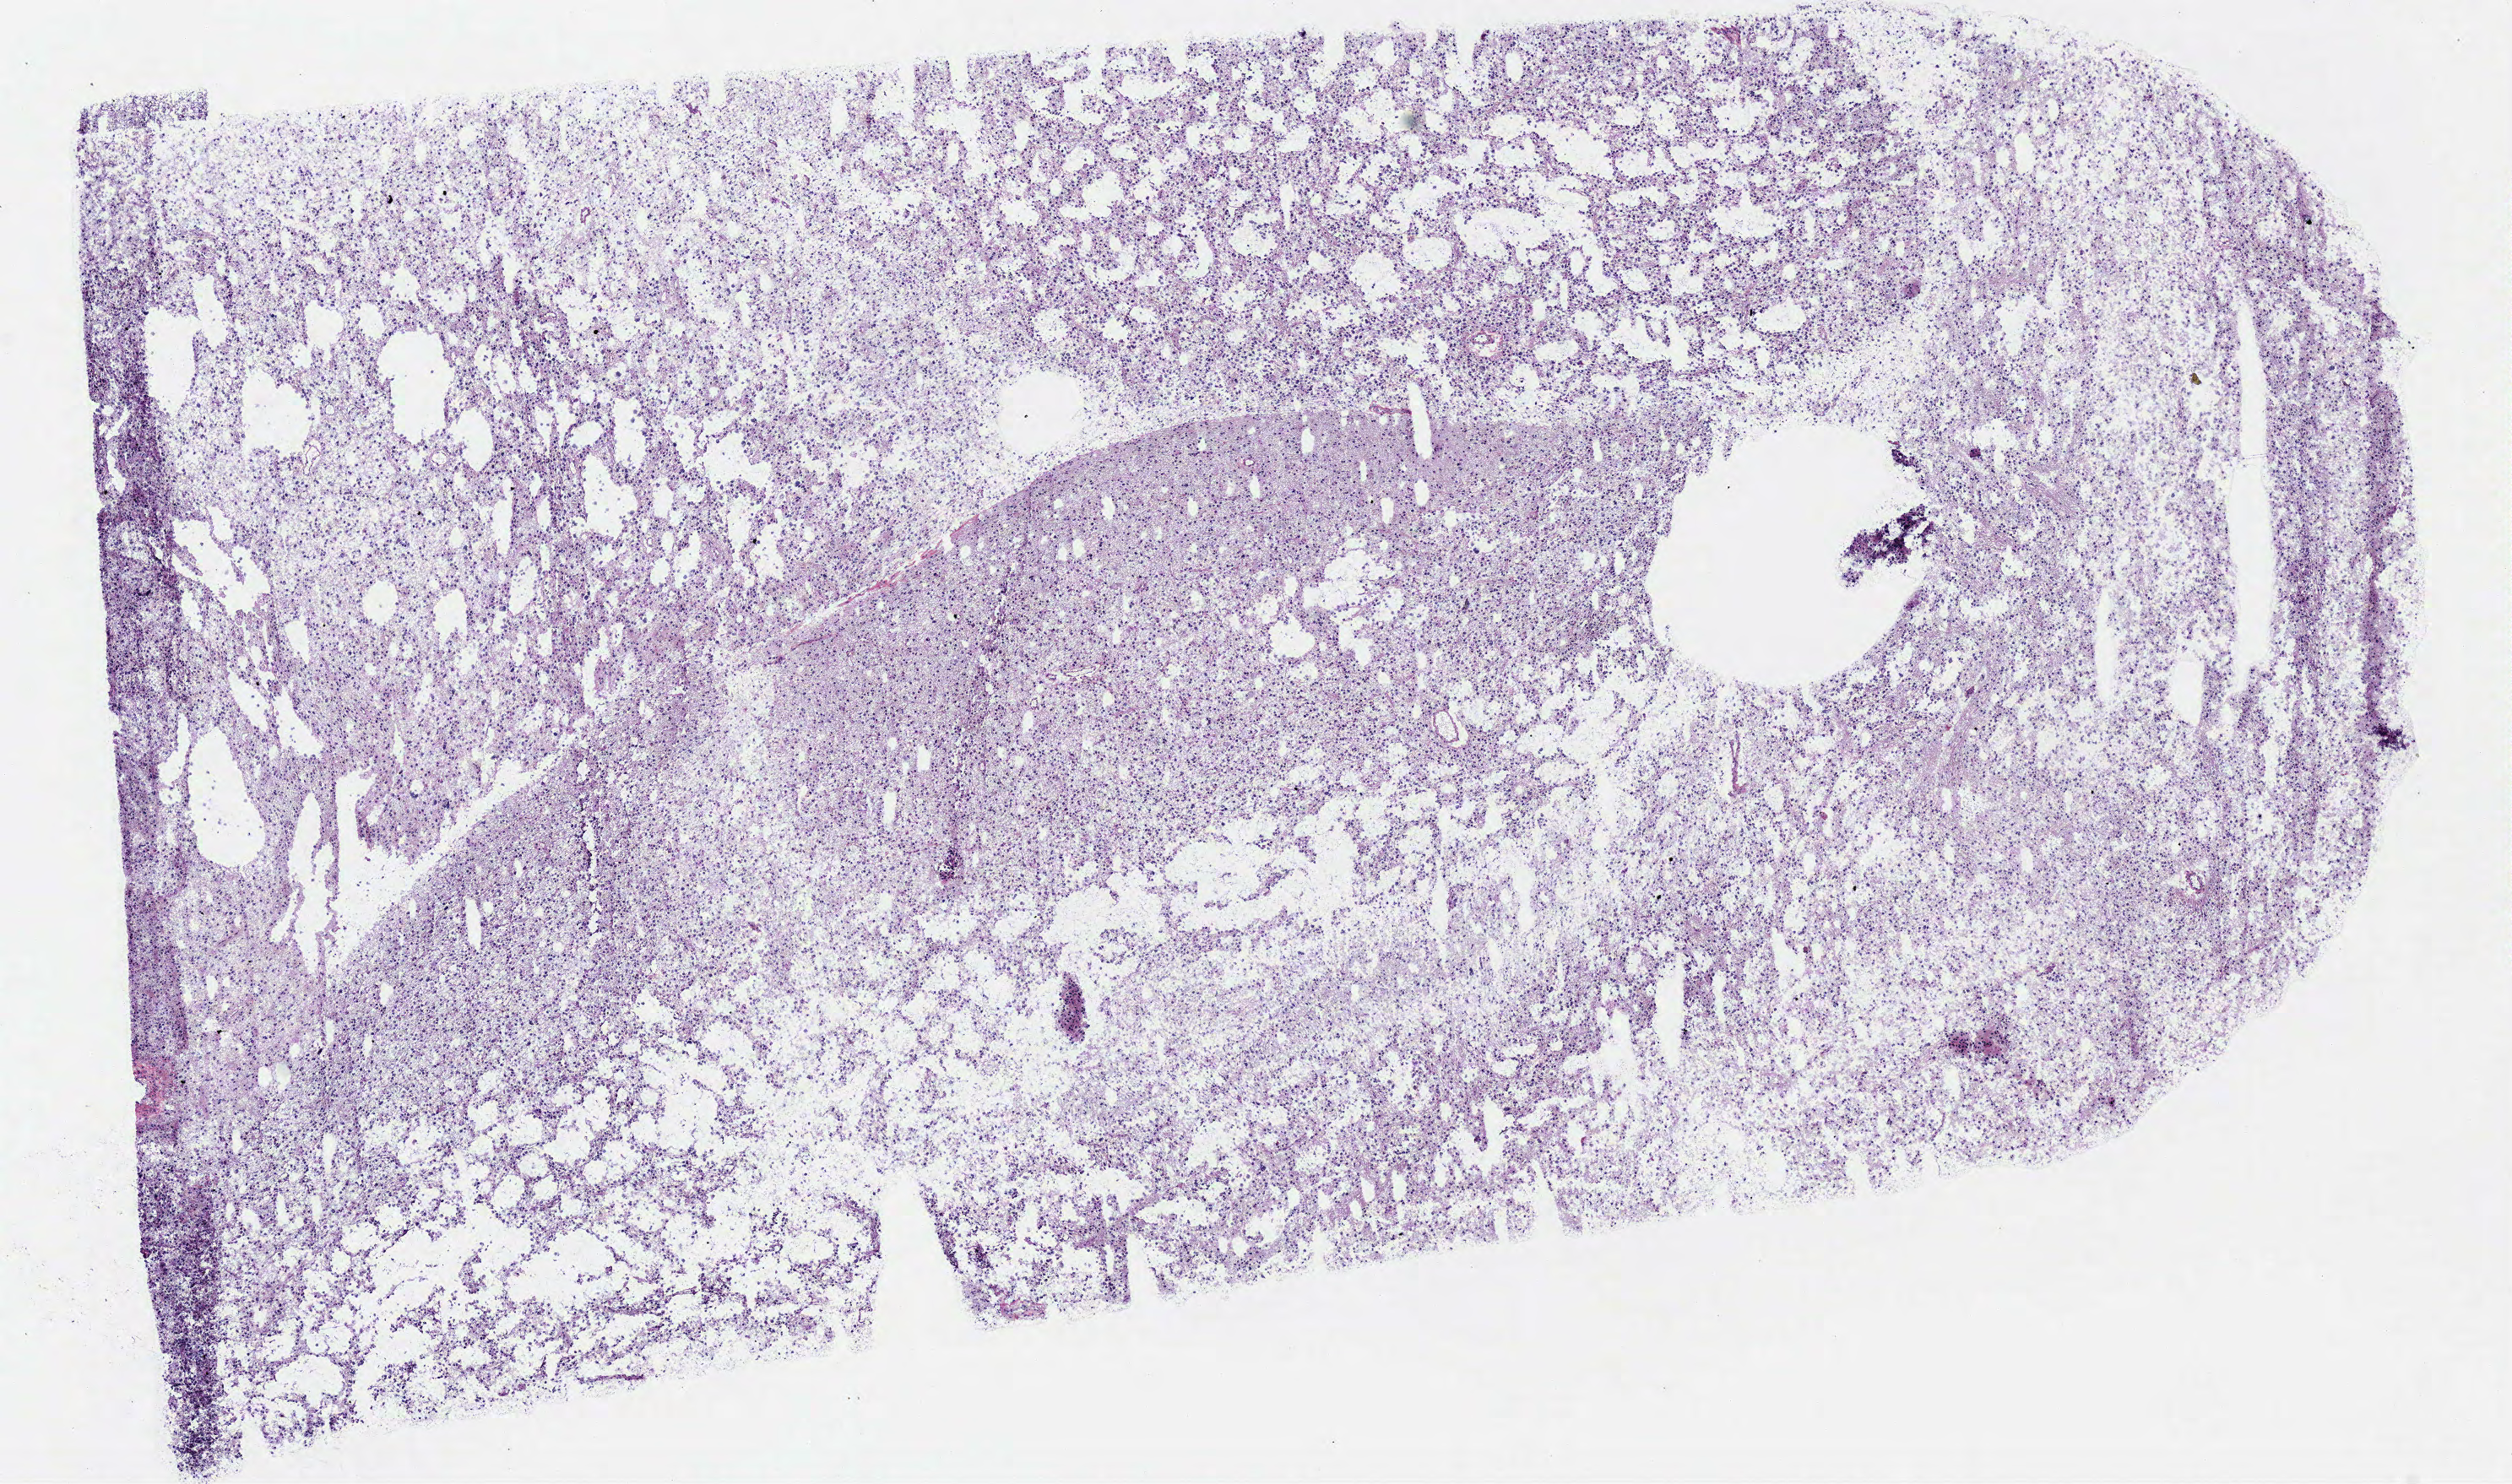
Hematoxylin and eosin (H&E) stained whole-slide image — shown as a low-resolution overview of the whole scanned area (about 11.7 x 6.9 mm, acquisition: 40x scan). Frozen section from the bottom of the tissue portion. Brain, primary tumour sample. Patient: female, age at initial diagnosis 37 years.
Pathologic diagnosis: Mixed glioma.